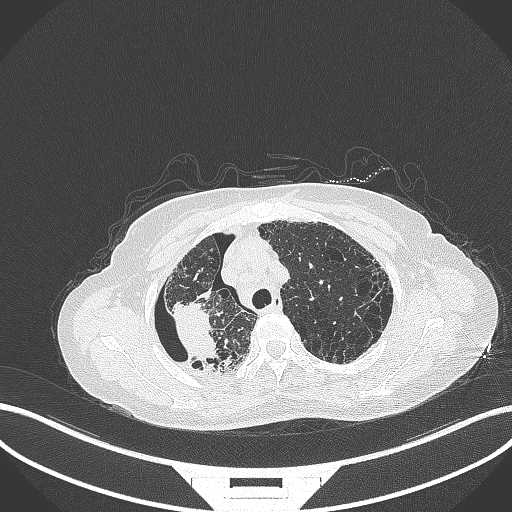
Chest CT, one axial slice. Reconstruction kernel B70f. 120 kVp. Lung window (W 1500 / L -600 HU). 1 mm slice thickness. 512 × 512 image matrix, field of view 400 × 400 mm. Female patient, age 64 years. Case-level facts recorded for this patient, not image findings: clinical TNM (as recorded): T3 N3 M0.
Outlined on this slice (rectangle marked by the reading radiologist):
- lung tumour (recorded histology: squamous cell carcinoma): bounding box (x1, y1, x2, y2) in pixels: (165, 293, 225, 366)